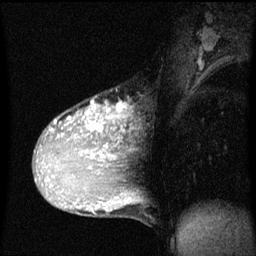
Breast MRI (dynamic contrast-enhanced), one sagittal slice; position 33 of 60 along the scan axis; dynamic contrast-enhanced series, image 2 of 3 at this slice position (ordered by acquisition); 1.5 T; TE 4.2 ms, TR 8 ms; 2 mm slice thickness; 256 × 256 image matrix, field of view 200 × 200 mm. Female patient, age 36 years.
Annotated regions visible in this slice (semi-automatic segmentation, software-assisted and operator-edited):
- analysis volume of interest (the breast-tissue region the enhancement analysis was run in; not a lesion): bounding box <33,100,127,169> (left, top, right, bottom; pixels)
- tumour enhancement mask (voxels above the 70 % enhancement threshold inside the analysis volume of interest): <51,100,127,165>